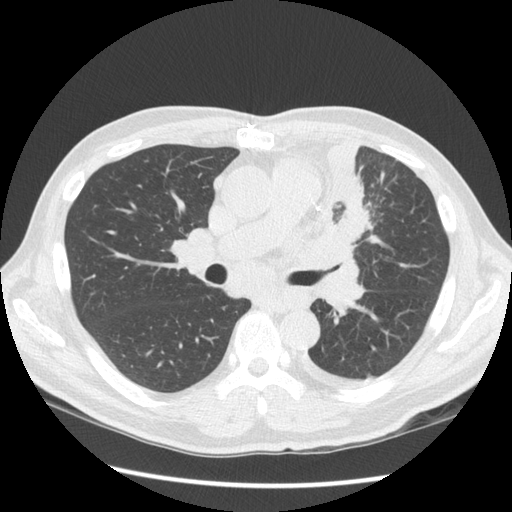
Low-dose screening chest CT, one axial slice. Slice 83 of 136 in the series (ordered by position). Reconstruction kernel STANDARD. 120 kVp. Lung window (W 1500 / L -600 HU). 2.5 mm slice thickness. 512 × 512 image matrix.
Outlined on this slice (outlined manually by an expert reader):
- lesion 1 (tumor, upper lobe of left lung): box from (x=301, y=137) to (x=370, y=270) px